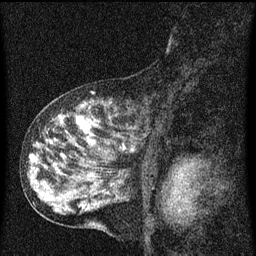
Breast MRI (dynamic contrast-enhanced), one sagittal slice. Slice 31 of 60 in the series (ordered by position). Dynamic contrast-enhanced series, image 2 of 3 at this slice position (ordered by acquisition). 1.5 T. TE 4.2 ms, TR 8 ms. 2 mm slice thickness. 256 × 256 image matrix, field of view 180 × 180 mm. Patient: female, 55 years.
Structures marked on this image (semi-automatic segmentation, software-assisted and operator-edited):
- analysis volume of interest (the breast-tissue region the enhancement analysis was run in; not a lesion): bounding box [x1, y1, x2, y2] px = [38, 92, 153, 159]
- tumour enhancement mask (voxels above the 70 % enhancement threshold inside the analysis volume of interest): [58, 118, 135, 151]